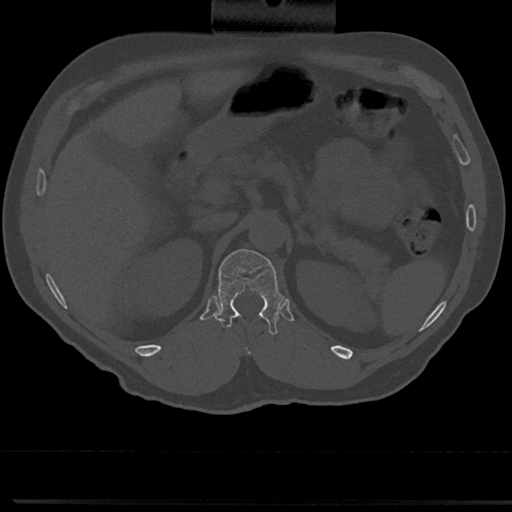
CT including the spine, one axial slice. Slice 152 of 817 in the series (ordered by position). Reconstruction kernel Br40s/3. 120 kVp. Bone window (W 1800 / L 400 HU). 0.5 mm slice thickness. 512 × 512 image matrix. Patient: male, 61 years. From the clinical record (not read from this slice): primary cancer: prostate.
Structures marked on this image (semi-automatically segmented with operator editing):
- T12 vertebra: box from (x=214, y=246) to (x=279, y=332) px